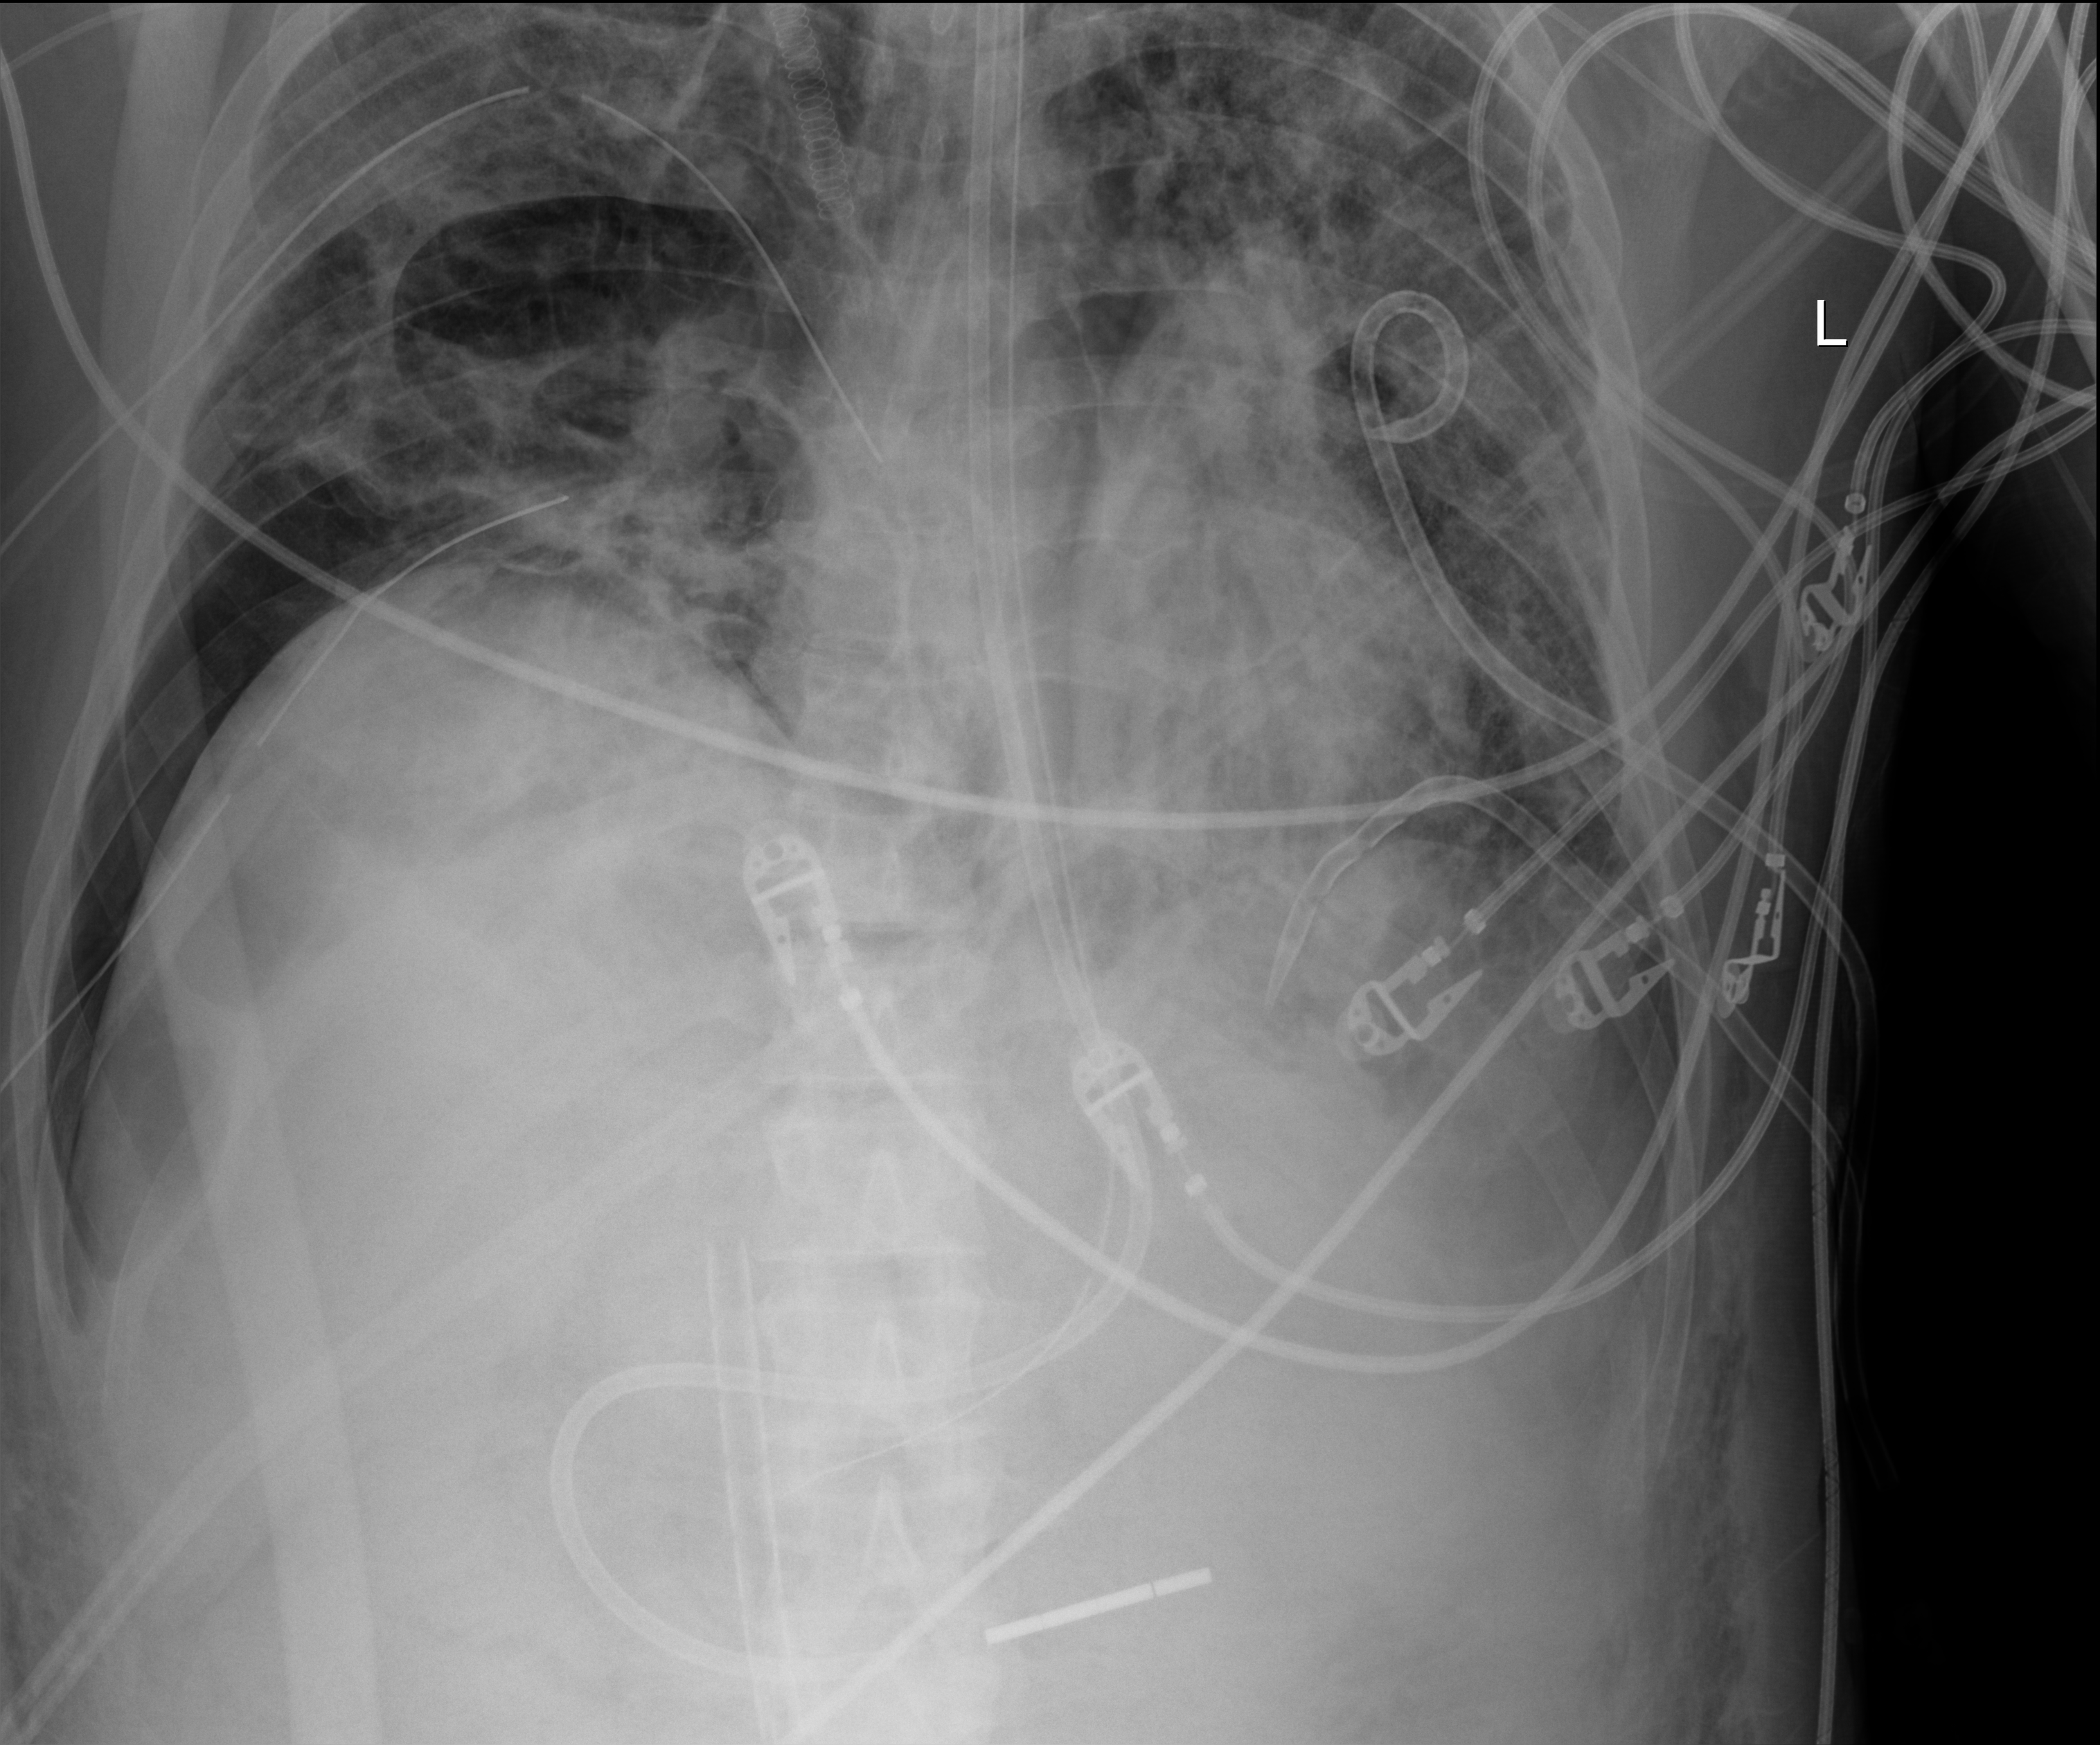
Chest X-ray; anteroposterior (AP) projection. Adult patient hospitalised with COVID-19, age 18–59 years.
Hospital-stay facts (about this admission, not read from this image; timing relative to this image not recorded): admitted to intensive care during this hospital stay: yes.